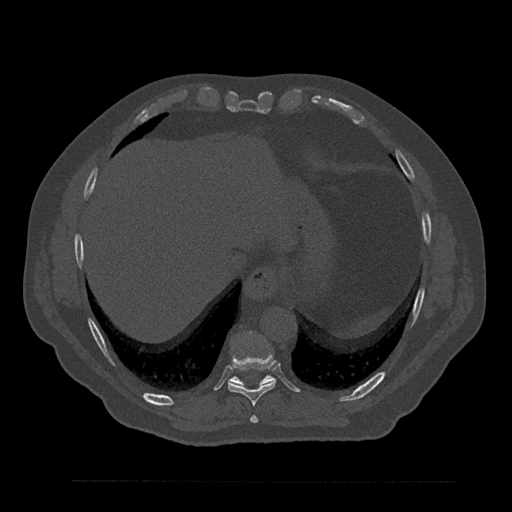
CT including the spine, one axial slice. Reconstruction kernel Br40s/3. Bone window (W 1800 / L 400 HU). 0.5 mm slice thickness. 512 × 512 image matrix, field of view 430 × 430 mm. Male patient, age 61 years. From the clinical record (not read from this slice): primary cancer: prostate.
Outlined on this slice (semi-automatically segmented with operator editing):
- T10 vertebra: box from (x=228, y=376) to (x=274, y=387) px
- T8 vertebra: (x=250, y=415)–(x=258, y=424)
- T9 vertebra: (x=228, y=353)–(x=276, y=406)